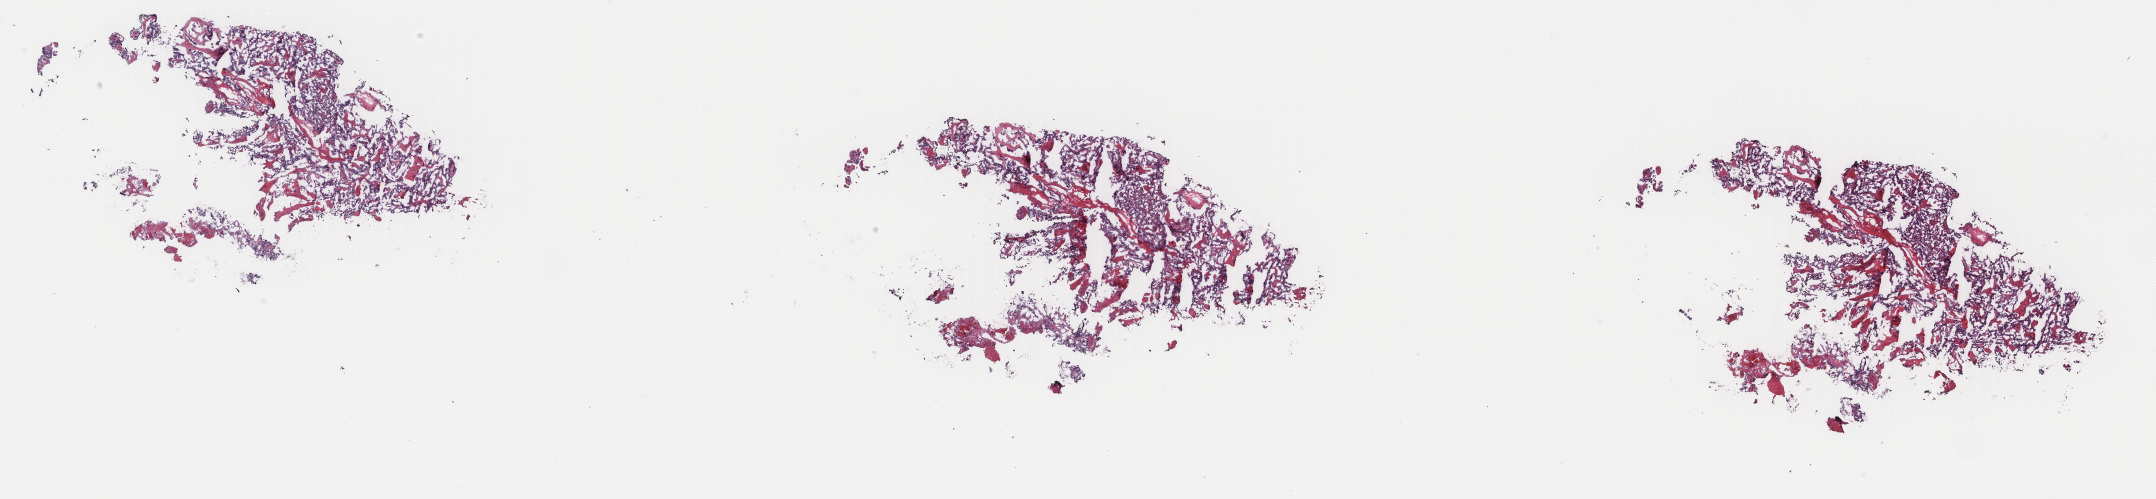
Whole-slide histology image, H&E — shown as a low-resolution overview of the whole scanned area (about 34.2 x 7.9 mm); frozen section; primary tumour sample from the thyroid. Male patient; age at initial diagnosis 35 years. Composition of this section per pathologist review: tumour cells 80%, tumour nuclei 80%, normal cells 0%, stromal cells 20%, necrosis 0%. Infiltration values recorded for this section: lymphocyte infiltration 3%, monocyte infiltration 0%, neutrophil infiltration 0%.
- histologic diagnosis: Papillary adenocarcinoma, NOS (thyroid gland)
- AJCC pathologic stage: I (6th edition)
- TNM: T3 N0 M0
- laterality: left